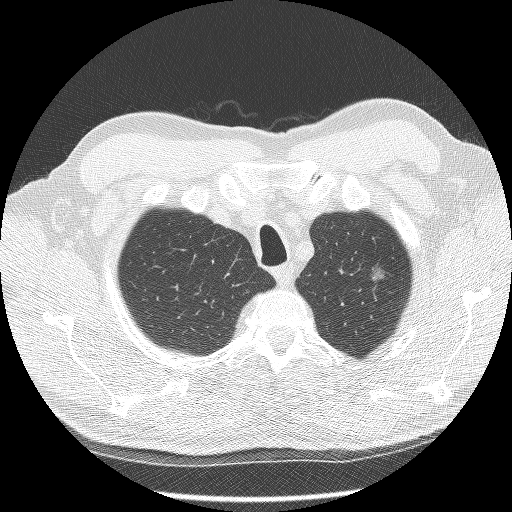
Chest CT (low-dose screening protocol), one axial image. Second screening round (one year after baseline). Lung window (W 1500 / L -600 HU). 2.5 mm slice thickness. Lung (sharp) reconstruction kernel (BONE). Slice 17 of 124 in the series. Male, age 60 years at enrolment. Former smoker at enrolment.
Lesion marked by an expert reader, bounding box [x1, y1, x2, y2] px = [345, 257, 399, 300]. The screening reader recorded 2 non-calcified nodules or masses ≥4 mm on this exam (right lower lobe, left upper lobe); which of them this box marks is not recorded. Participant outcome: lung cancer diagnosed 448 days after this screen (after the third annual screen) — bronchiolo-alveolar carcinoma, non-mucinous, left upper lobe, well differentiated (G1), stage IA (AJCC 6th edition), 16 mm at pathology.